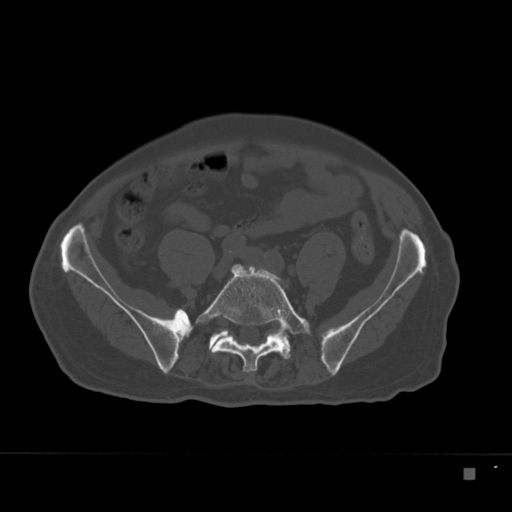
CT including the spine, one axial slice. Position 21 of 332 along the scan axis. Reconstruction kernel Br40s. Bone window (W 1800 / L 400 HU). 1.5 mm slice thickness. 512 × 512 image matrix, field of view 389 × 389 mm. Patient: male, 72 years. From the clinical record (not read from this slice): primary cancer: skeletal.
Outlined on this slice (semi-automatically segmented with operator editing):
- L5 vertebra: box from (x=196, y=264) to (x=311, y=372) px